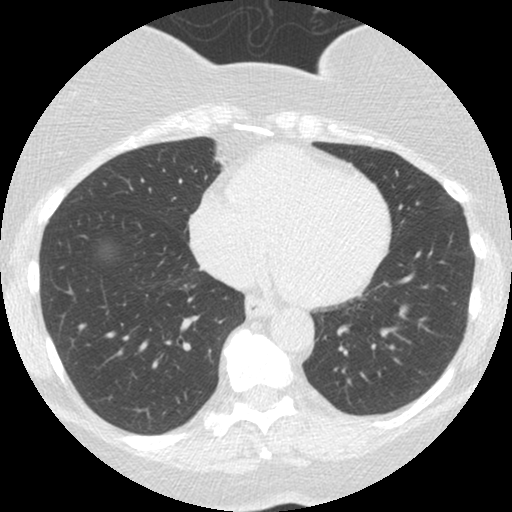
Low-dose screening chest CT, one axial slice; position 60 of 167 along the scan axis; 120 kVp; lung window (W 1500 / L -600 HU); 512 × 512 image matrix, field of view 300 × 300 mm.
Structures marked on this image (manually delineated by an expert):
- lesion 1 (tumor, lower lobe of left lung): bounding box <400,309,405,316> (left, top, right, bottom; pixels)